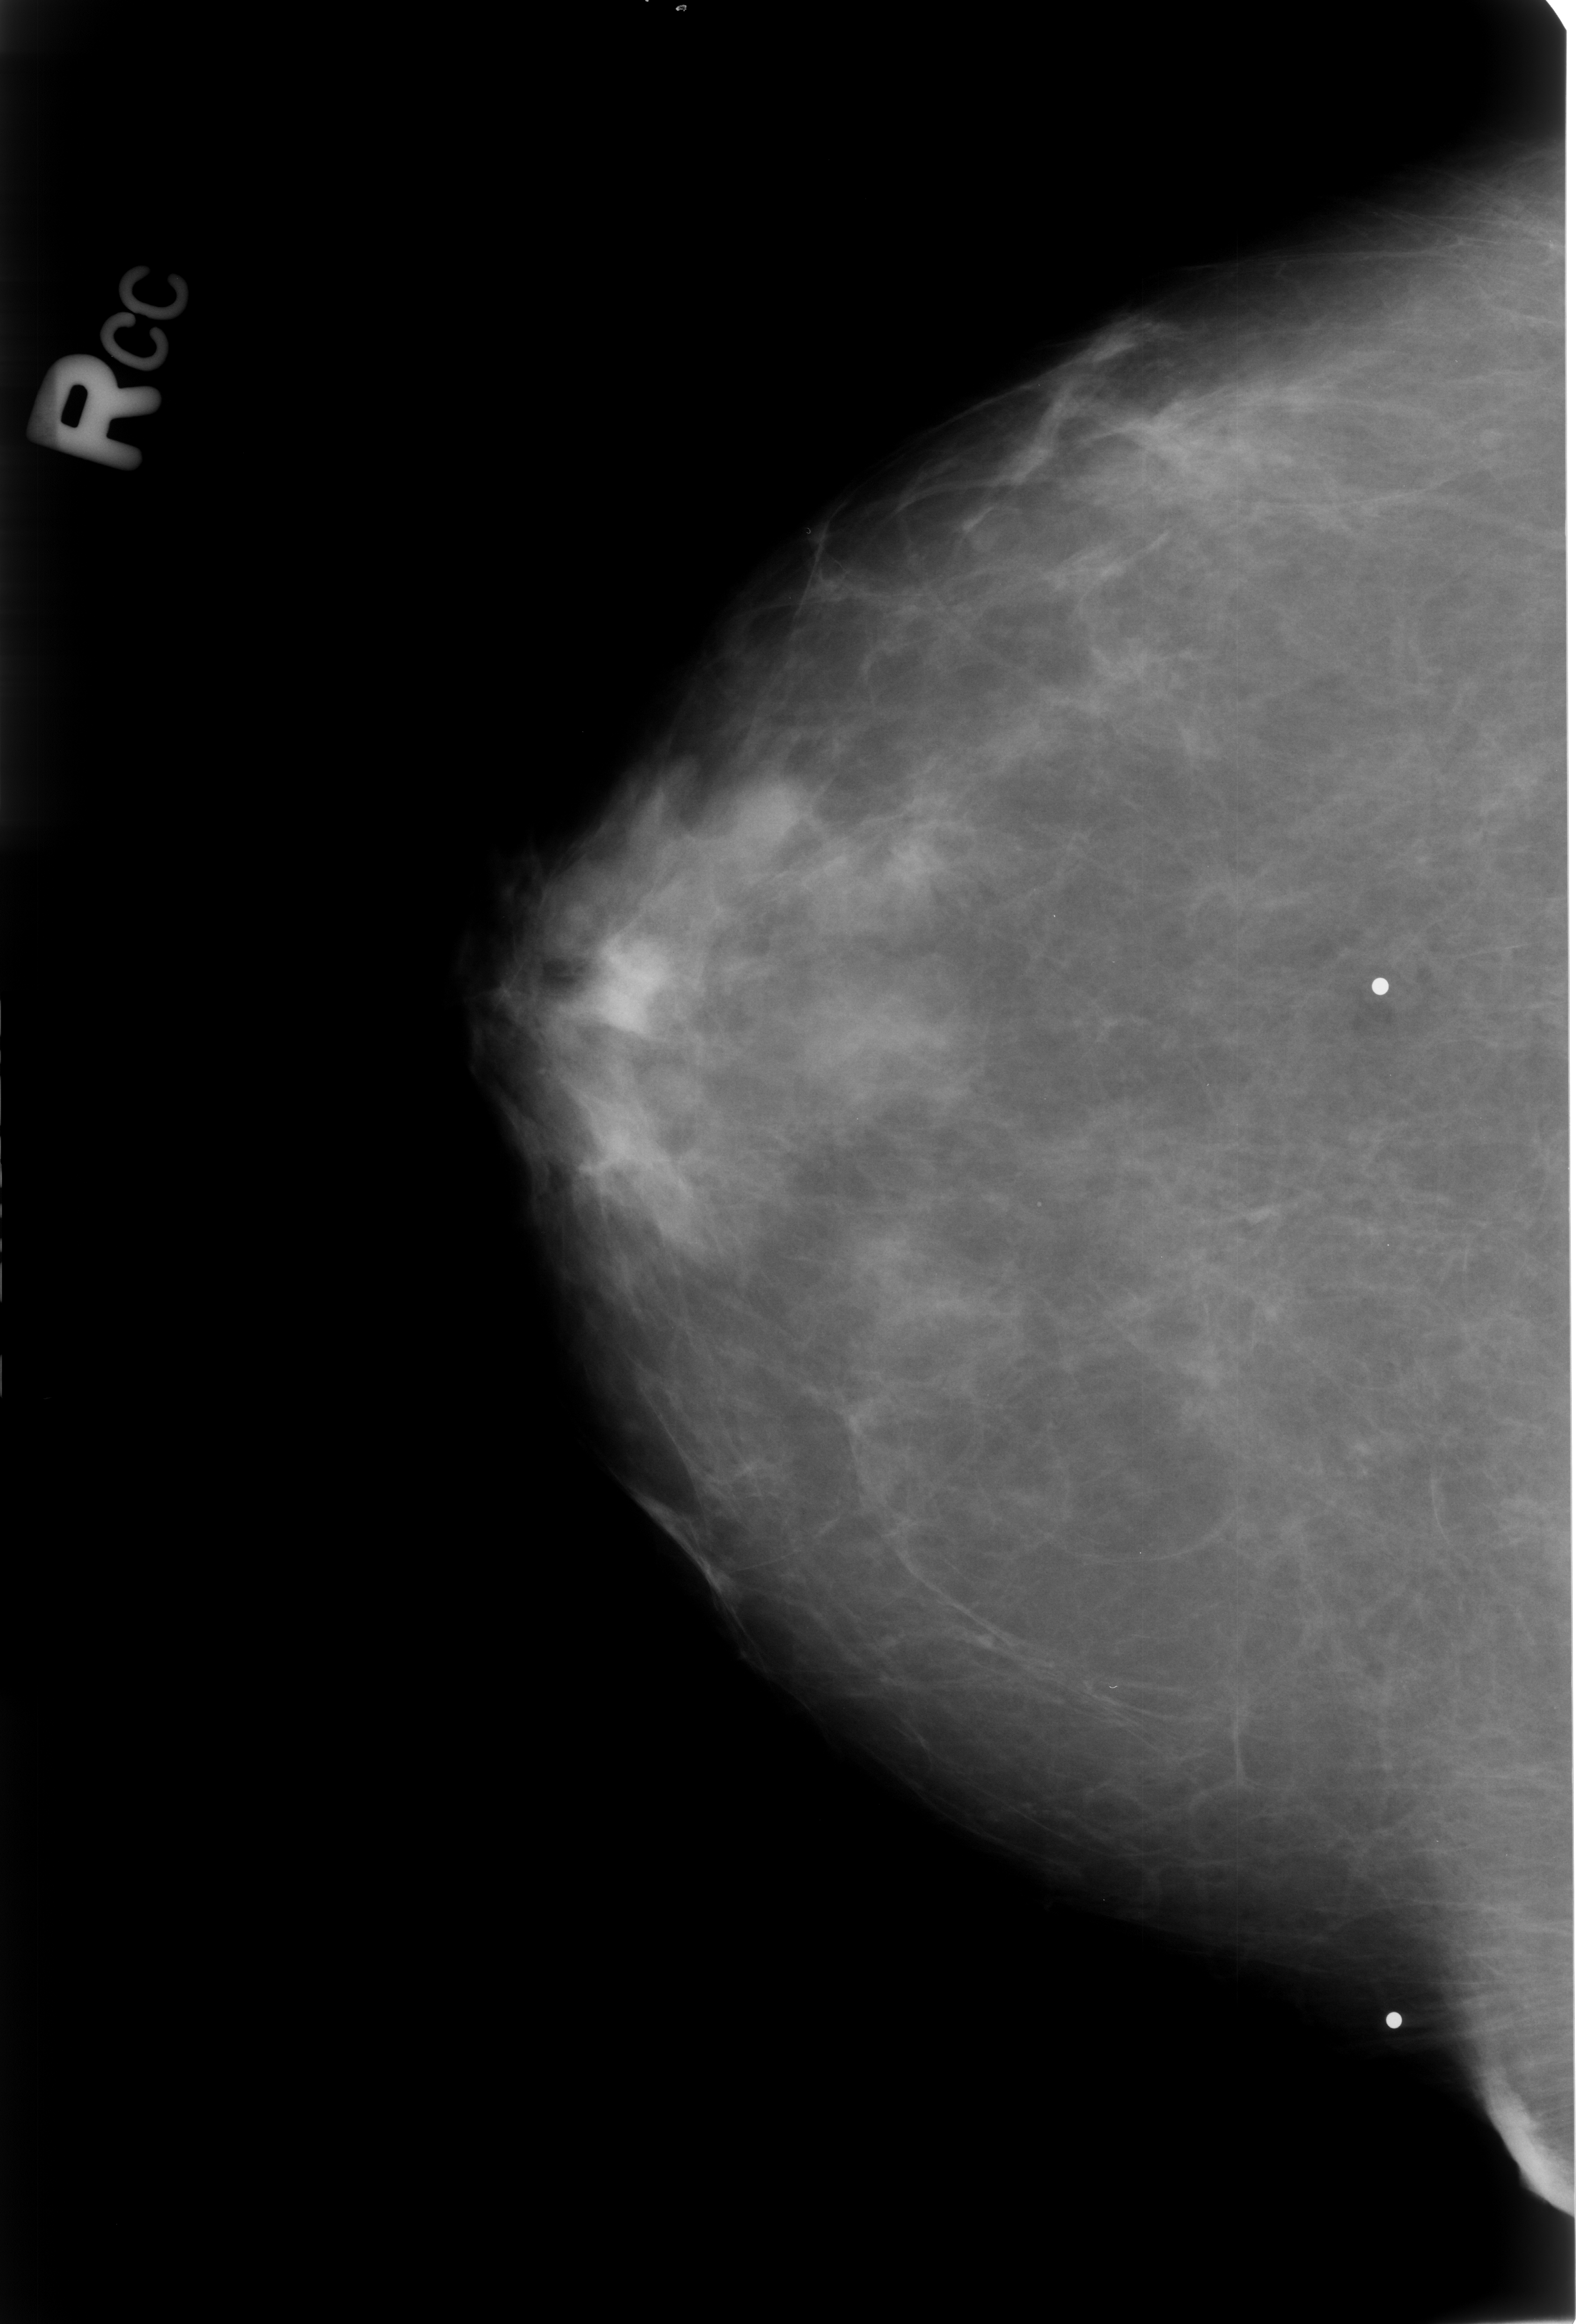
Scanned film-screen mammogram; right breast; craniocaudal (CC) view; BI-RADS breast density category 2 (scale 1–4); 1576 × 2324 image matrix.
Expert-marked regions of interest on this image (one box per marked abnormality):
- calcifications, morphology punctate; BI-RADS assessment category 2; outcome (as recorded, no biopsy): benign without callback (not worked up further): bounding box [x1, y1, x2, y2] px = [1007, 1174, 1081, 1236]